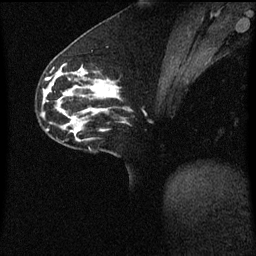
Breast MRI (dynamic contrast-enhanced), one sagittal slice. Slice 23 of 60 in the series (ordered by position). Dynamic contrast-enhanced series, image 2 of 3 at this slice position (ordered by acquisition). 1.5 T. TE 4.2 ms, TR 8.4 ms. 2 mm slice thickness. 256 × 256 image matrix, field of view 200 × 200 mm. Female patient, age 33 years. From the clinical record (not read from this slice): setting: breast cancer imaged before/during neoadjuvant chemotherapy; receptor status: triple-negative.
Outlined on this slice (semi-automatic segmentation, software-assisted and operator-edited):
- analysis volume of interest (the breast-tissue region the enhancement analysis was run in; not a lesion): bounding box [x1, y1, x2, y2] px = [76, 66, 120, 113]
- tumour enhancement mask (voxels above the 70 % enhancement threshold inside the analysis volume of interest): [88, 82, 113, 97]